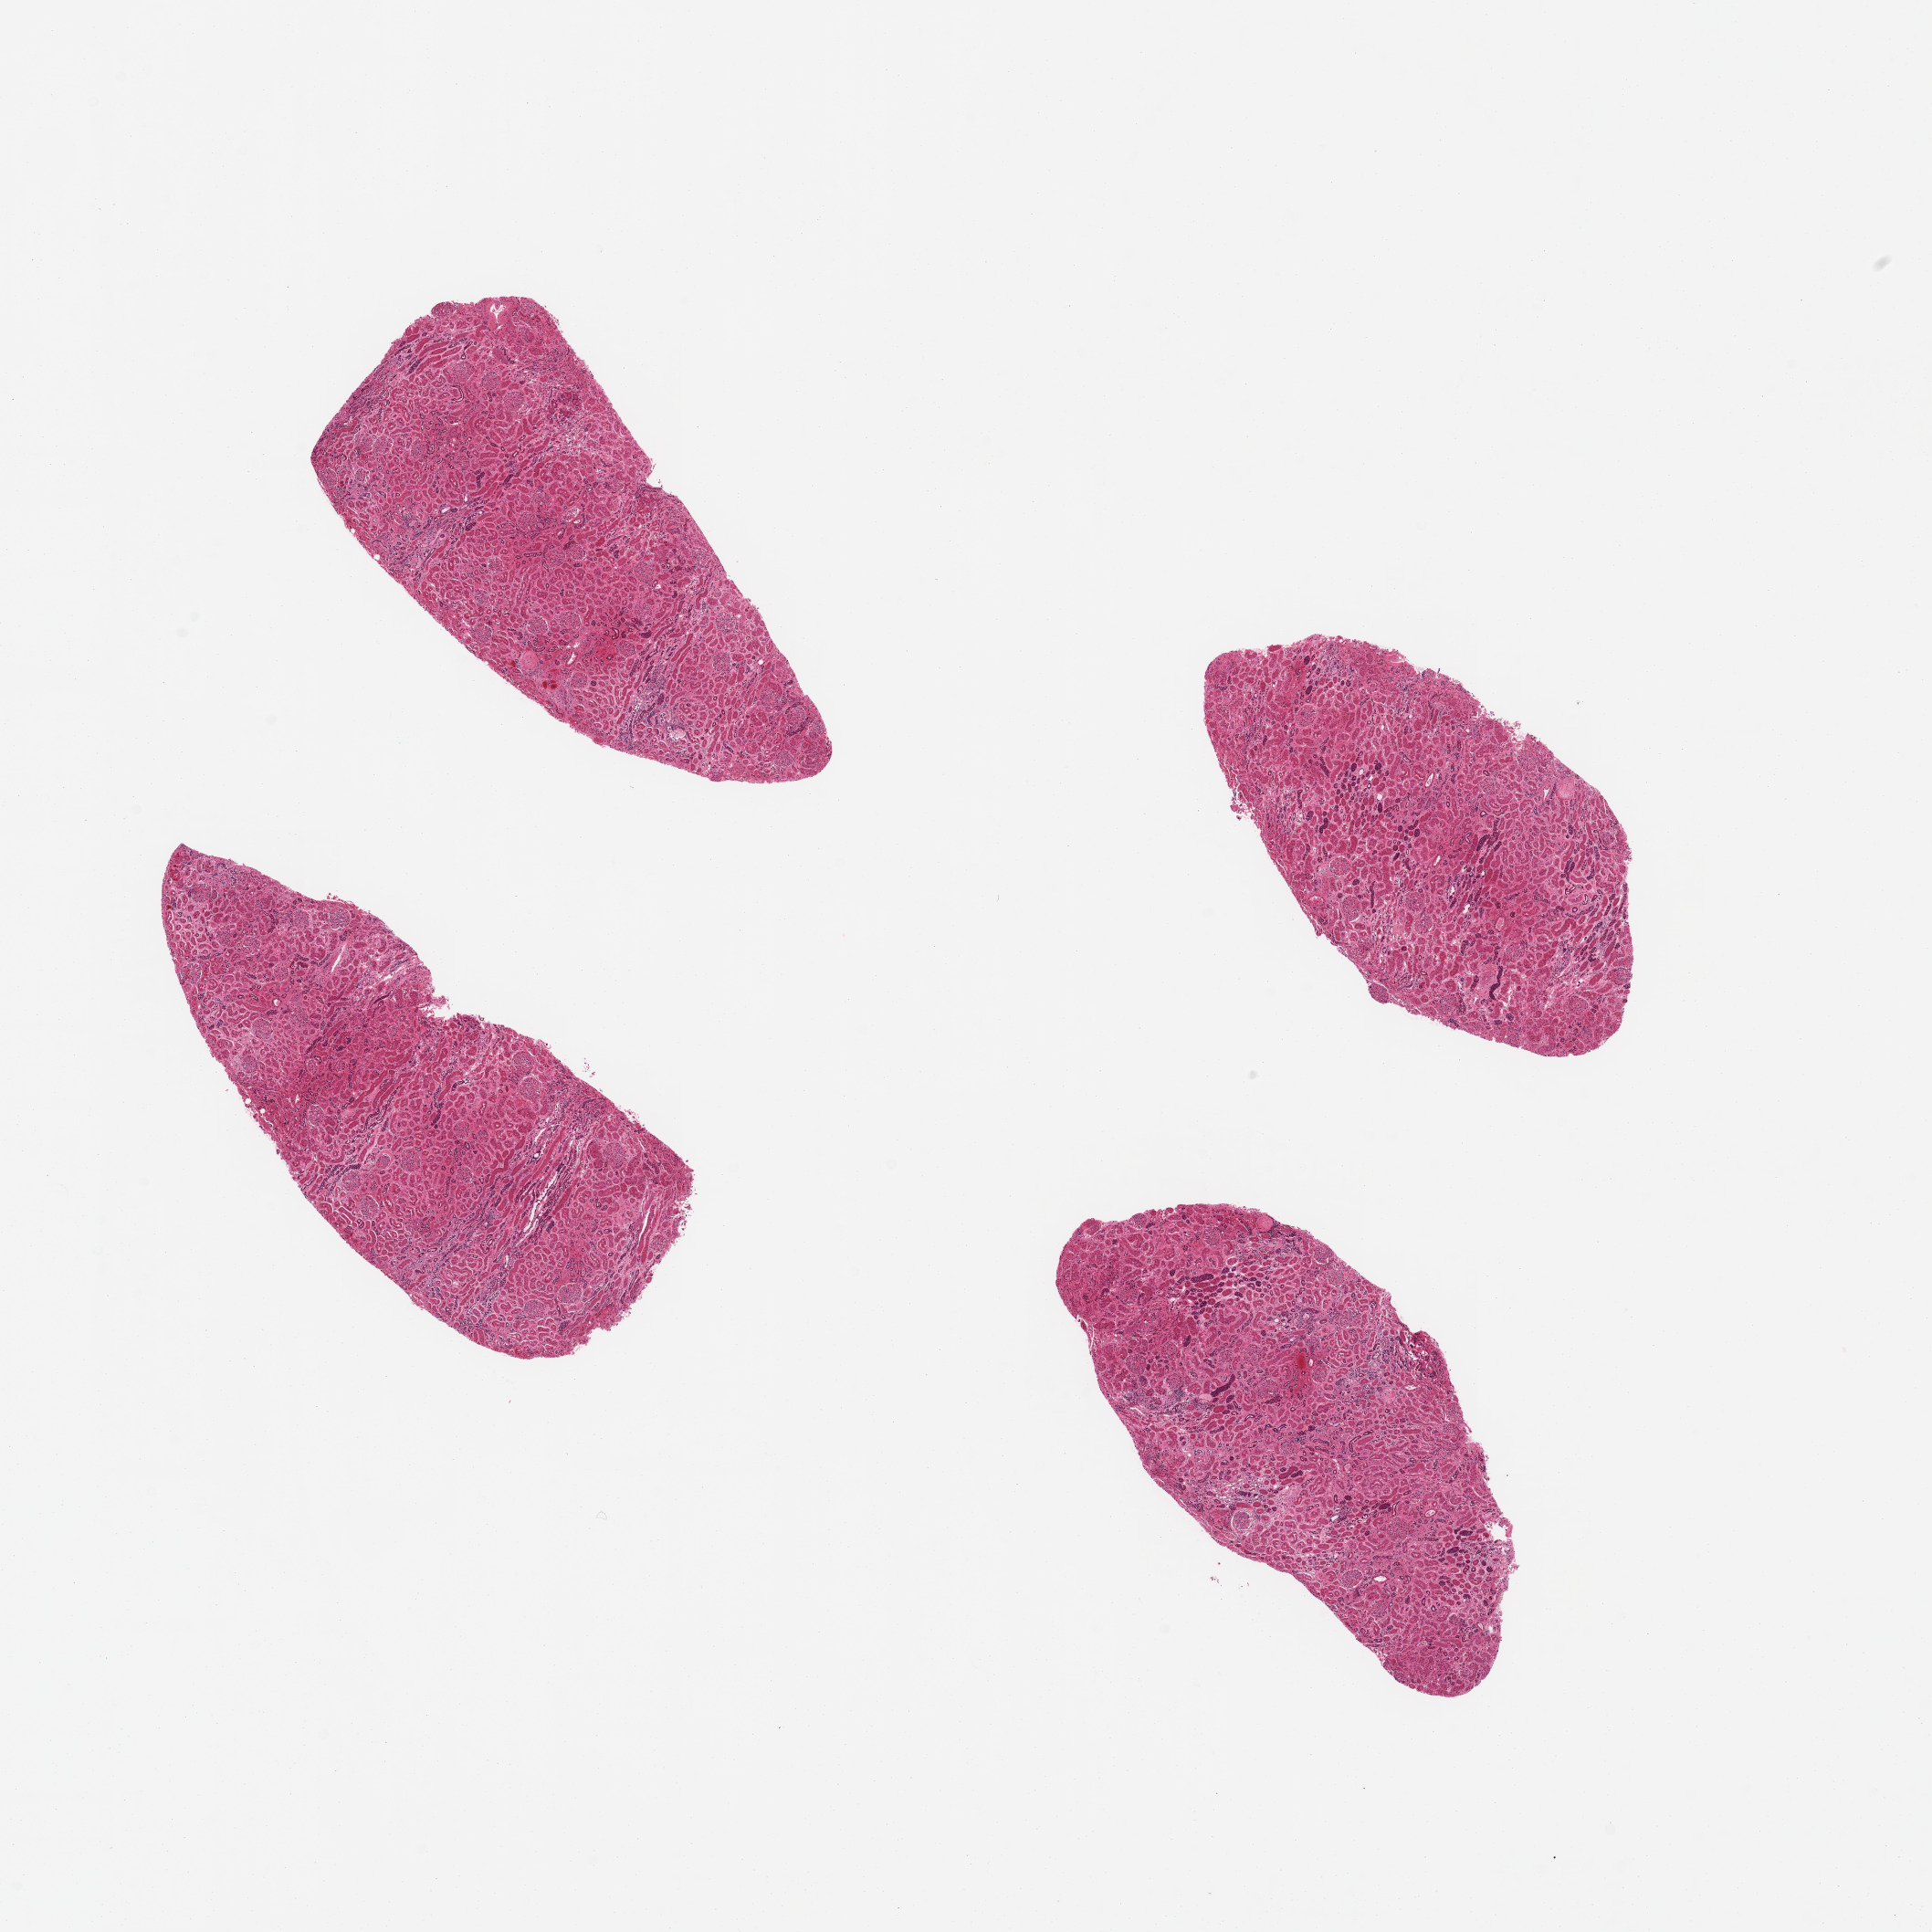
Digitized hematoxylin and eosin (H&E)-stained section — whole scanned area (about 16.7 x 16.7 mm) shown as a low-resolution overview, PAXgene-fixed paraffin-embedded (PFPE) section, section of renal cortex (target tissue), tissue donor sample. Donor sex: female.
- reviewer comment on this tissue sample: 4 pieces; tubules autolyzed, glomeruli intact; no sign of active or chronic disease